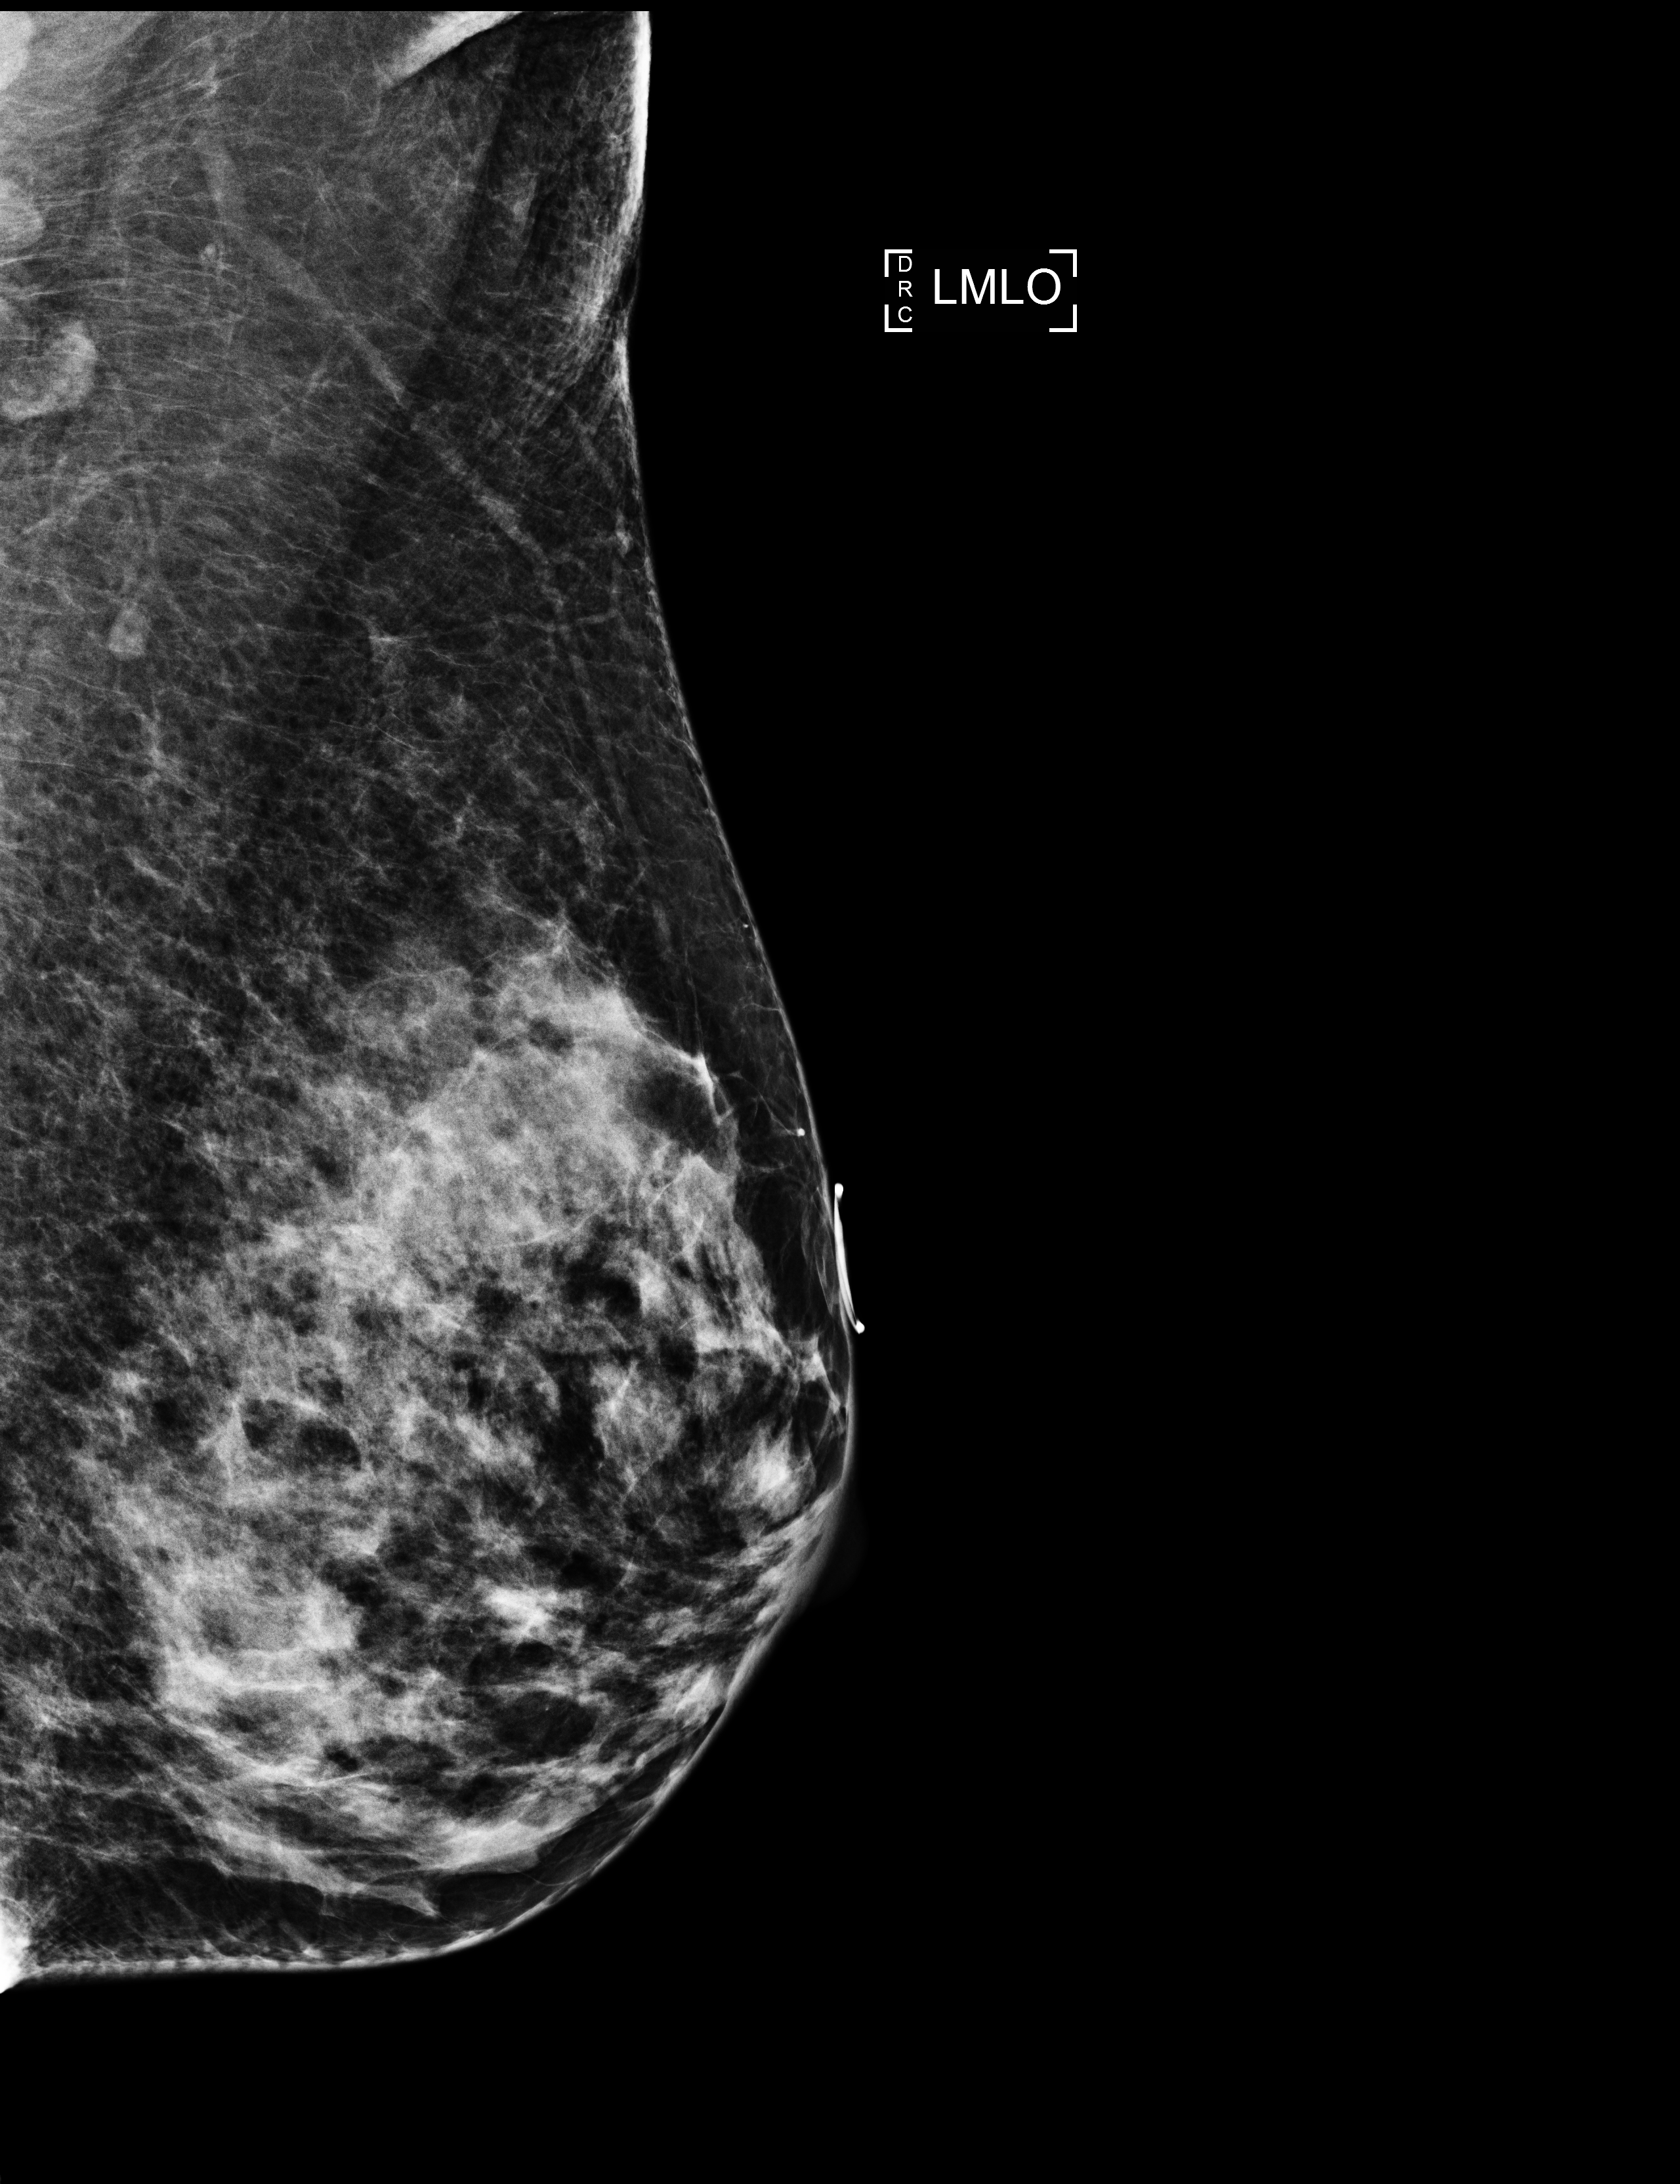
Full-field digital mammogram (FFDM); left breast; medio-lateral oblique projection; annual screening mammography examination; compressed breast thickness 53 mm. Female patient, age 60 years.
BI-RADS breast density category at the screening exam (both breasts, scale 1–4): 3. Final BI-RADS category for the screening round (tomosynthesis exam, both breasts): category 1. Recall: no recall after this screen.